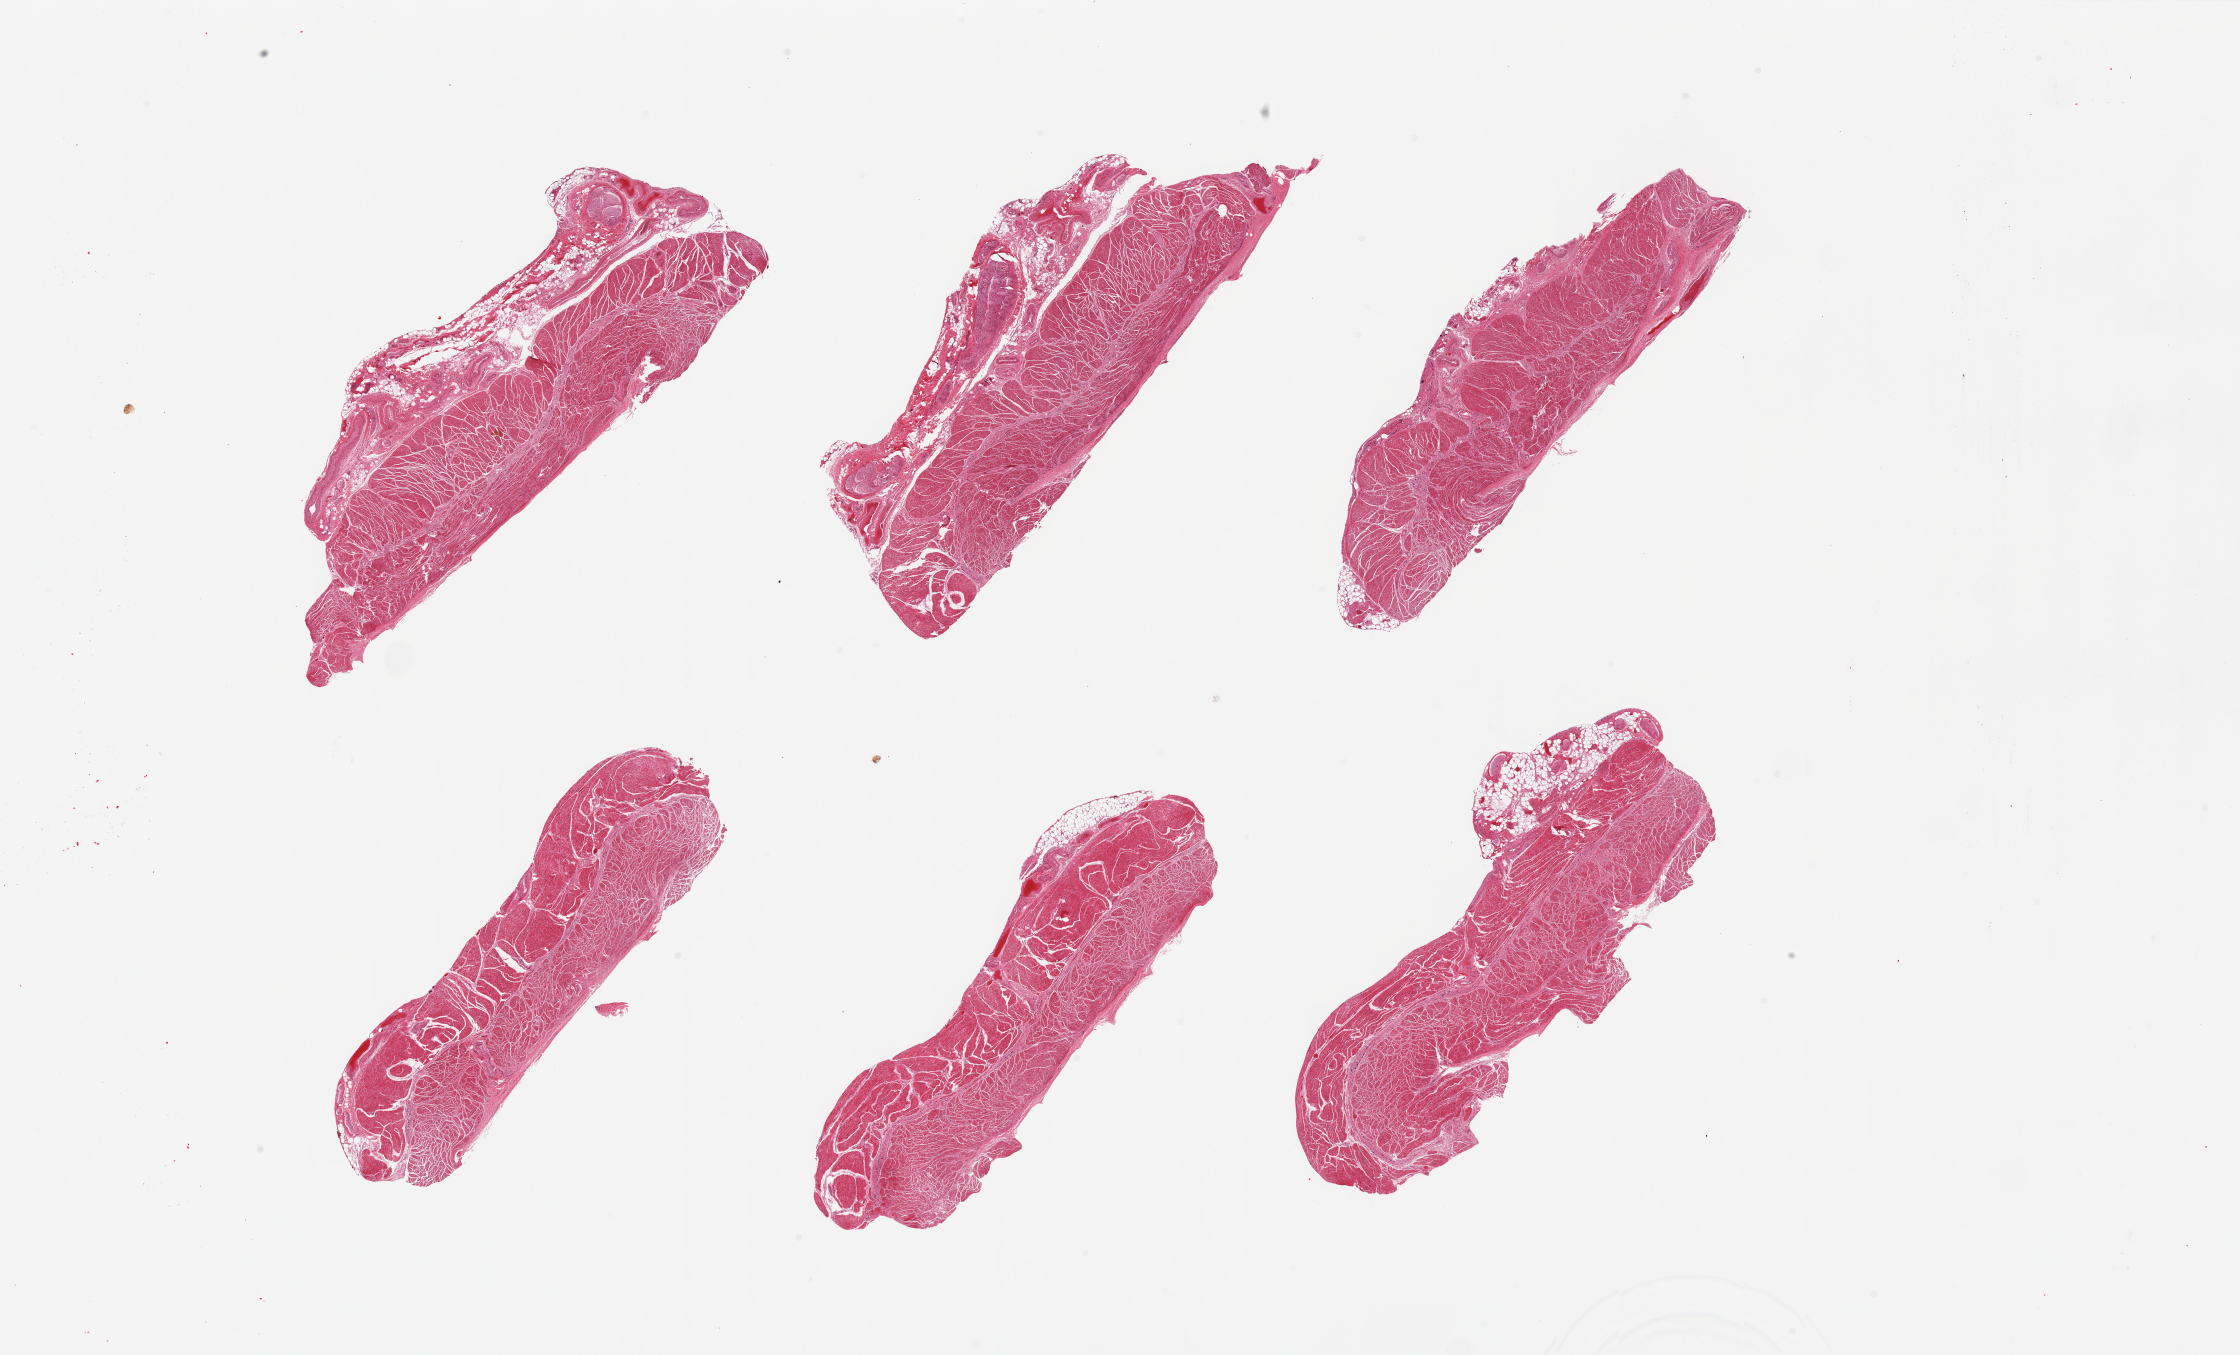
Whole-slide image, hematoxylin and eosin (H&E) stain — shown as a low-resolution overview of the whole scanned area (about 35.4 x 21.4 mm). PAXgene-fixed, paraffin-embedded tissue. Sampled site (target tissue): esophageal muscle. Tissue donor sample. Donor sex: male.
- review note (as recorded): 6 pieces; up to 1.6mm external fat